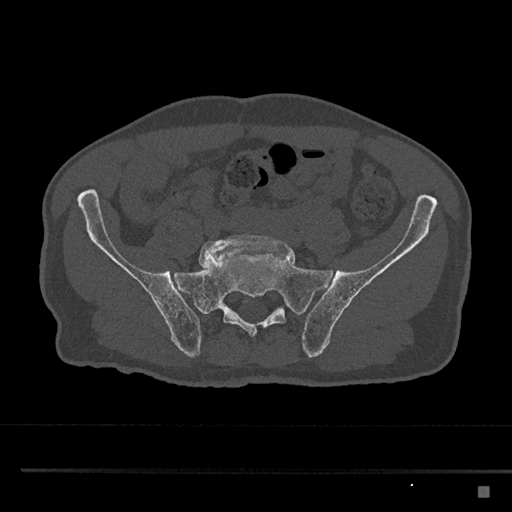
CT including the spine, one axial slice; slice 532 of 797 in the series (ordered by position); reconstruction kernel Br40s/3; bone window (W 1800 / L 400 HU); 0.5 mm slice thickness; 512 × 512 image matrix. Patient: male, 59 years. From the clinical record (not read from this slice): primary cancer: prostate.
Annotated regions visible in this slice (semi-automatically segmented with operator editing):
- L5 vertebra: box from (x=198, y=234) to (x=288, y=268) px